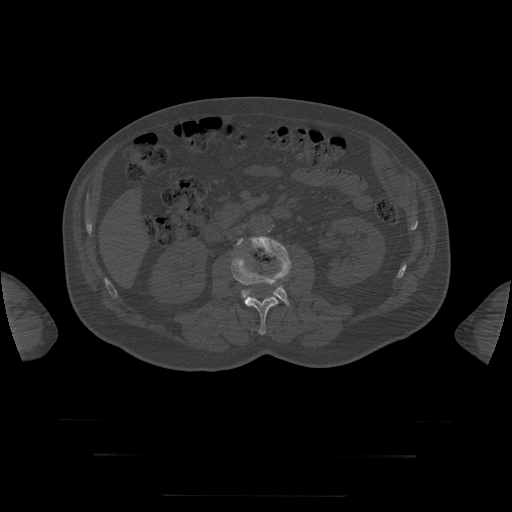
CT including the spine, one axial slice; slice 14 of 397 in the series (ordered by position); reconstruction kernel STANDARD; 120 kVp; bone window (W 1800 / L 400 HU); 1.25 mm slice thickness; 512 × 512 image matrix, field of view 510 × 510 mm. Patient age 73 years. Case-level facts recorded for this patient, not image findings: primary cancer: prostate.
Annotated regions visible in this slice (semi-automatic segmentation, software-assisted and operator-edited):
- L3 vertebra: bounding box [x1, y1, x2, y2] px = [237, 236, 292, 306]